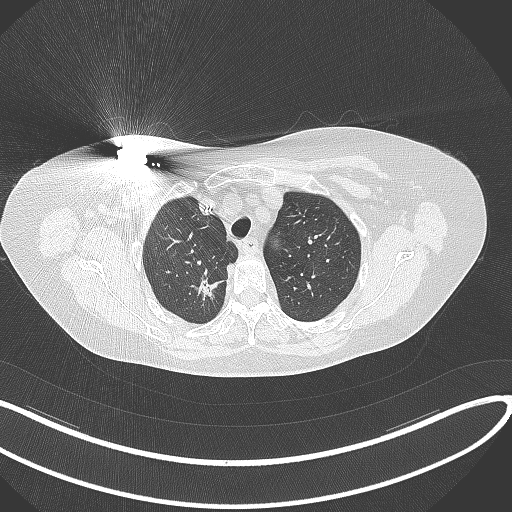
Chest CT, one axial slice. Slice 270 of 316 in the series (ordered by position). Reconstruction kernel B70f. 120 kVp. Lung window (W 1500 / L -600 HU). 1 mm slice thickness. 512 × 512 image matrix, field of view 400 × 400 mm. Female patient, age 72 years. From the clinical record (not read from this slice): clinical TNM (as recorded): T1c N0 M0.
Annotated regions visible in this slice (rectangle marked by the reading radiologist):
- lung tumour (recorded histology: adenocarcinoma): bounding box (x1, y1, x2, y2) in pixels: (189, 269, 223, 306)